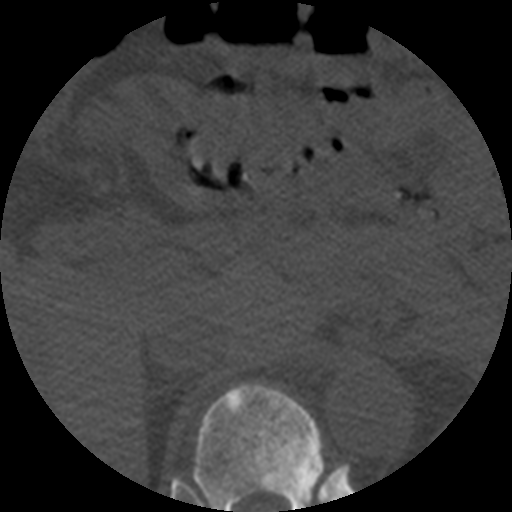
CT including the spine, one axial slice. Position 247 of 508 along the scan axis. 120 kVp. Bone window (W 1800 / L 400 HU). 1.25 mm slice thickness. 512 × 512 image matrix. Patient age 57 years. Case-level facts recorded for this patient, not image findings: primary cancer: prostate.
Annotated regions visible in this slice (semi-automatically segmented with operator editing):
- T11 vertebra: bounding box [x1, y1, x2, y2] px = [192, 383, 325, 512]